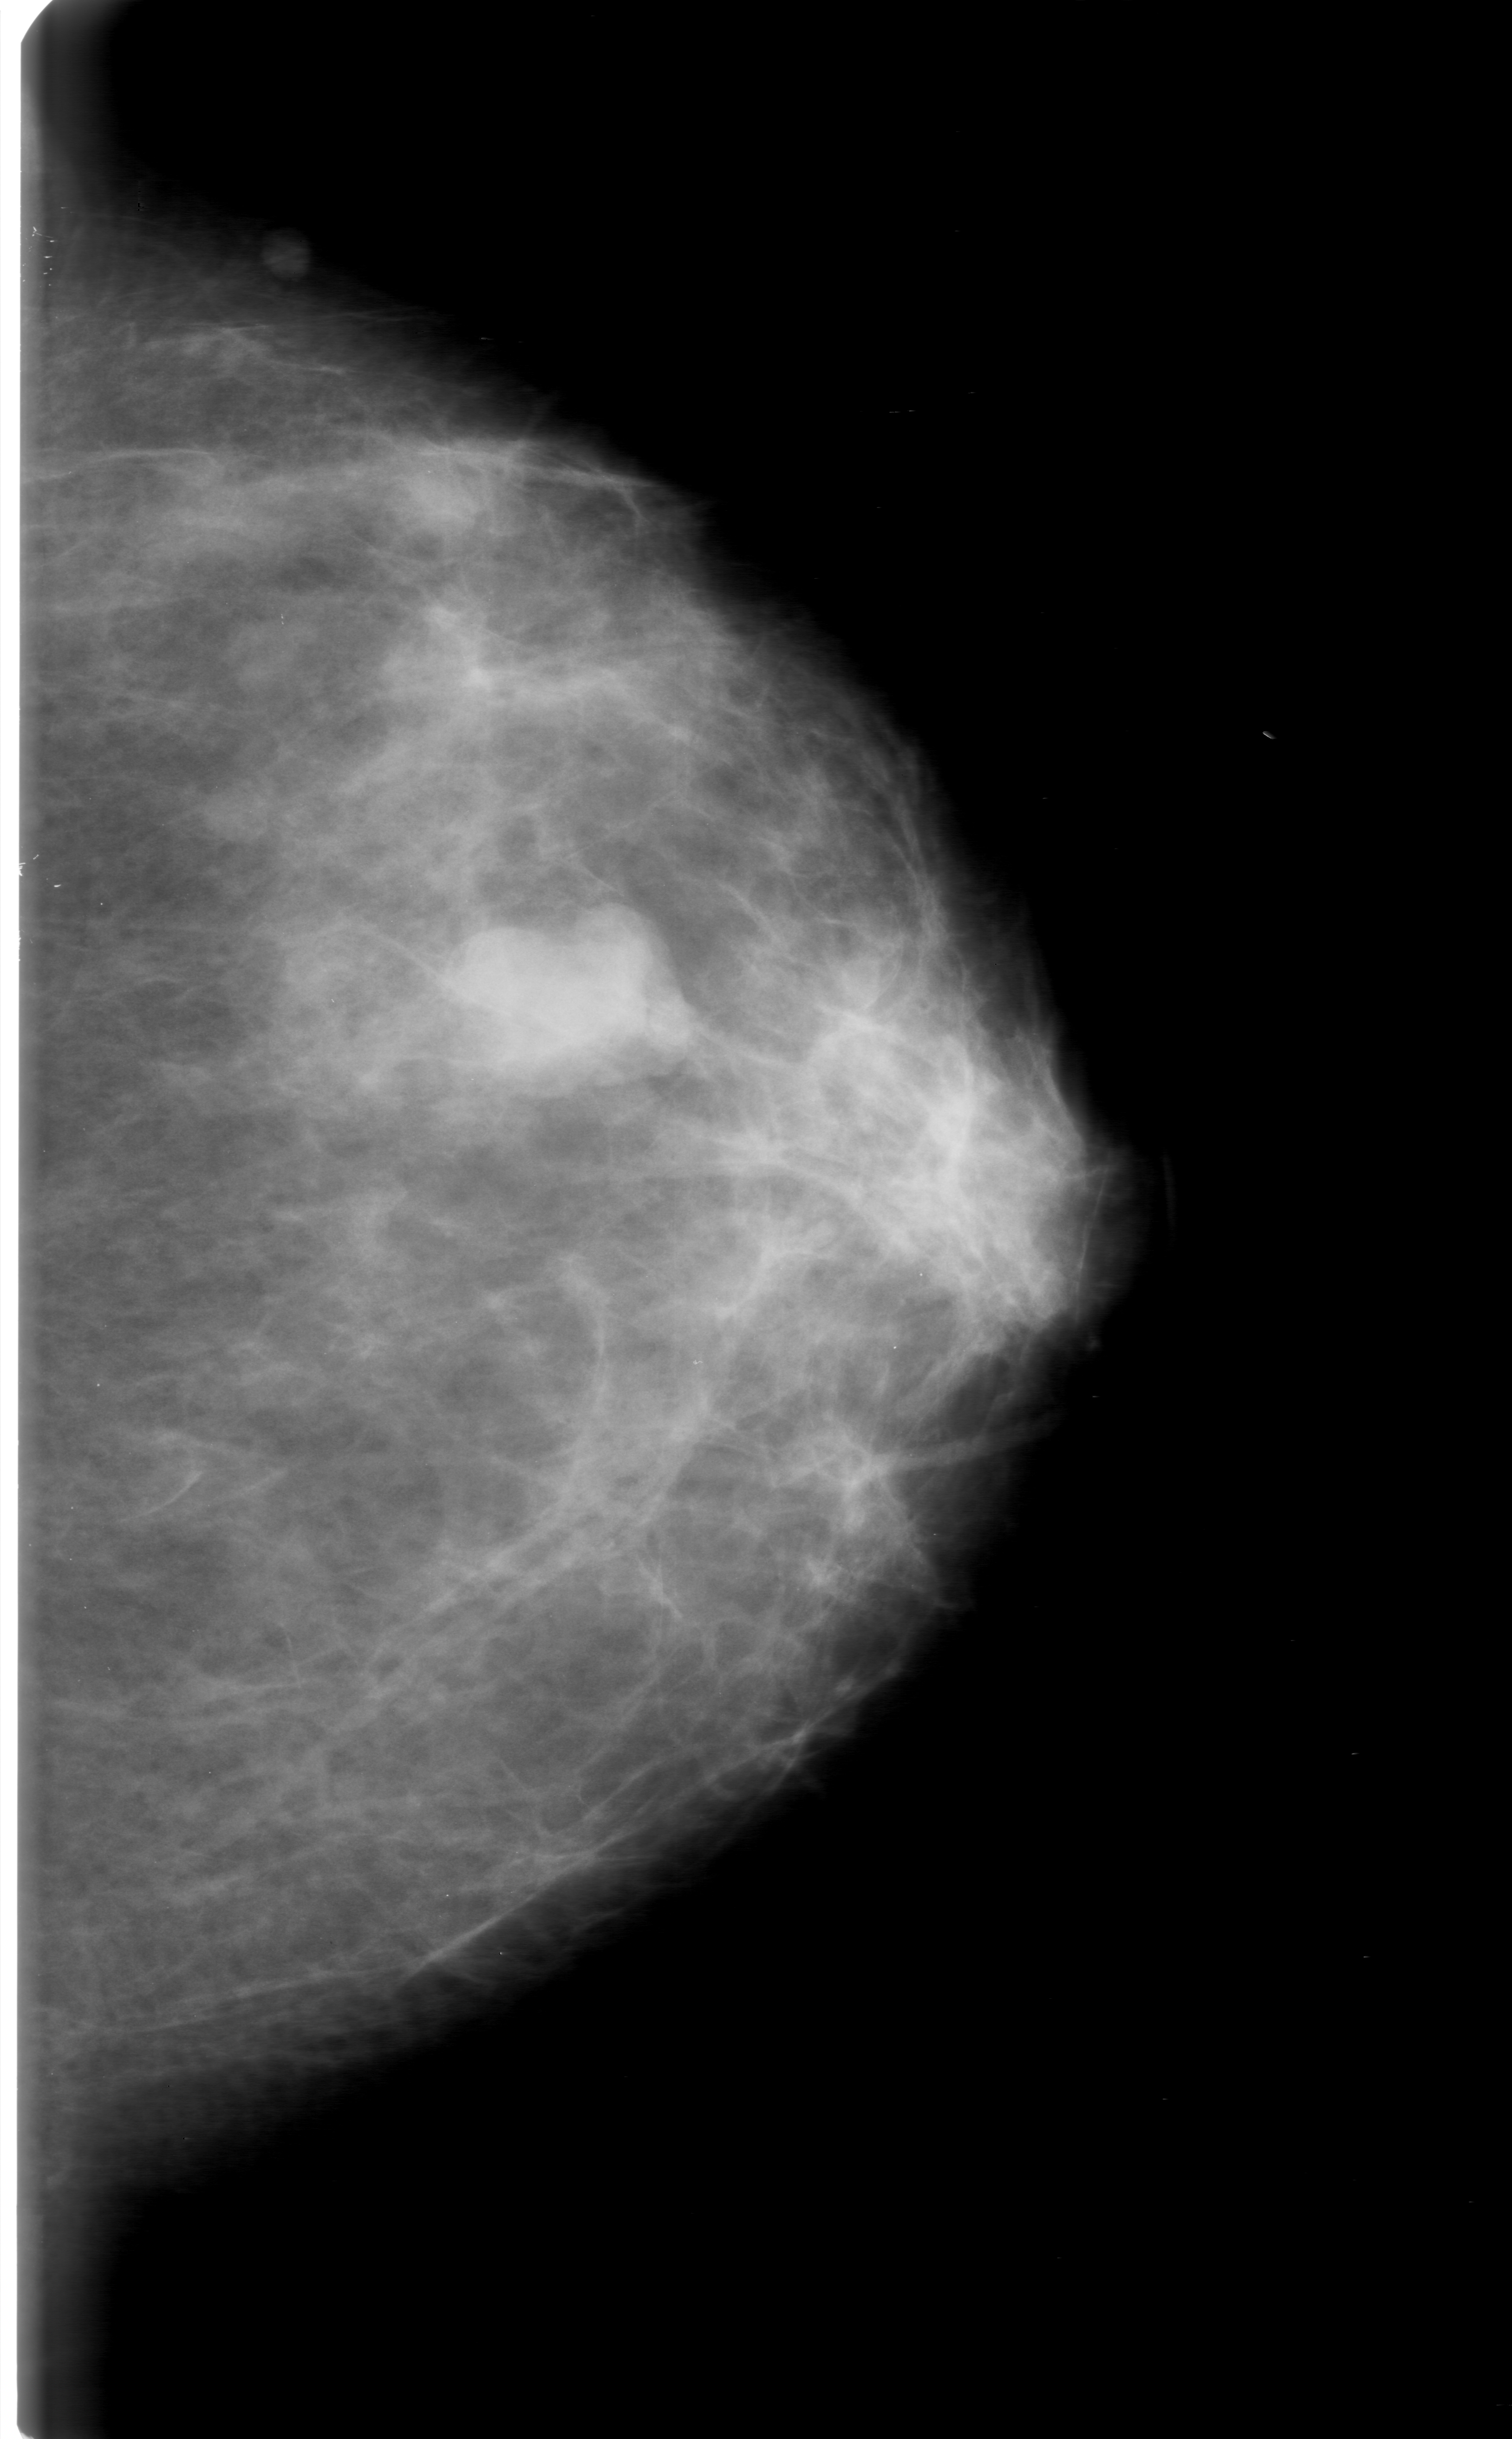
Scanned film-screen mammogram, left breast, CC view, BI-RADS breast density category 3 (scale 1–4).
Radiologist-marked abnormalities on this image: mass, shape lobulated, margins circumscribed; BI-RADS assessment category 0; subtlety rating 5 on a 1 (subtle) to 5 (obvious) scale; pathology (as recorded): benign.